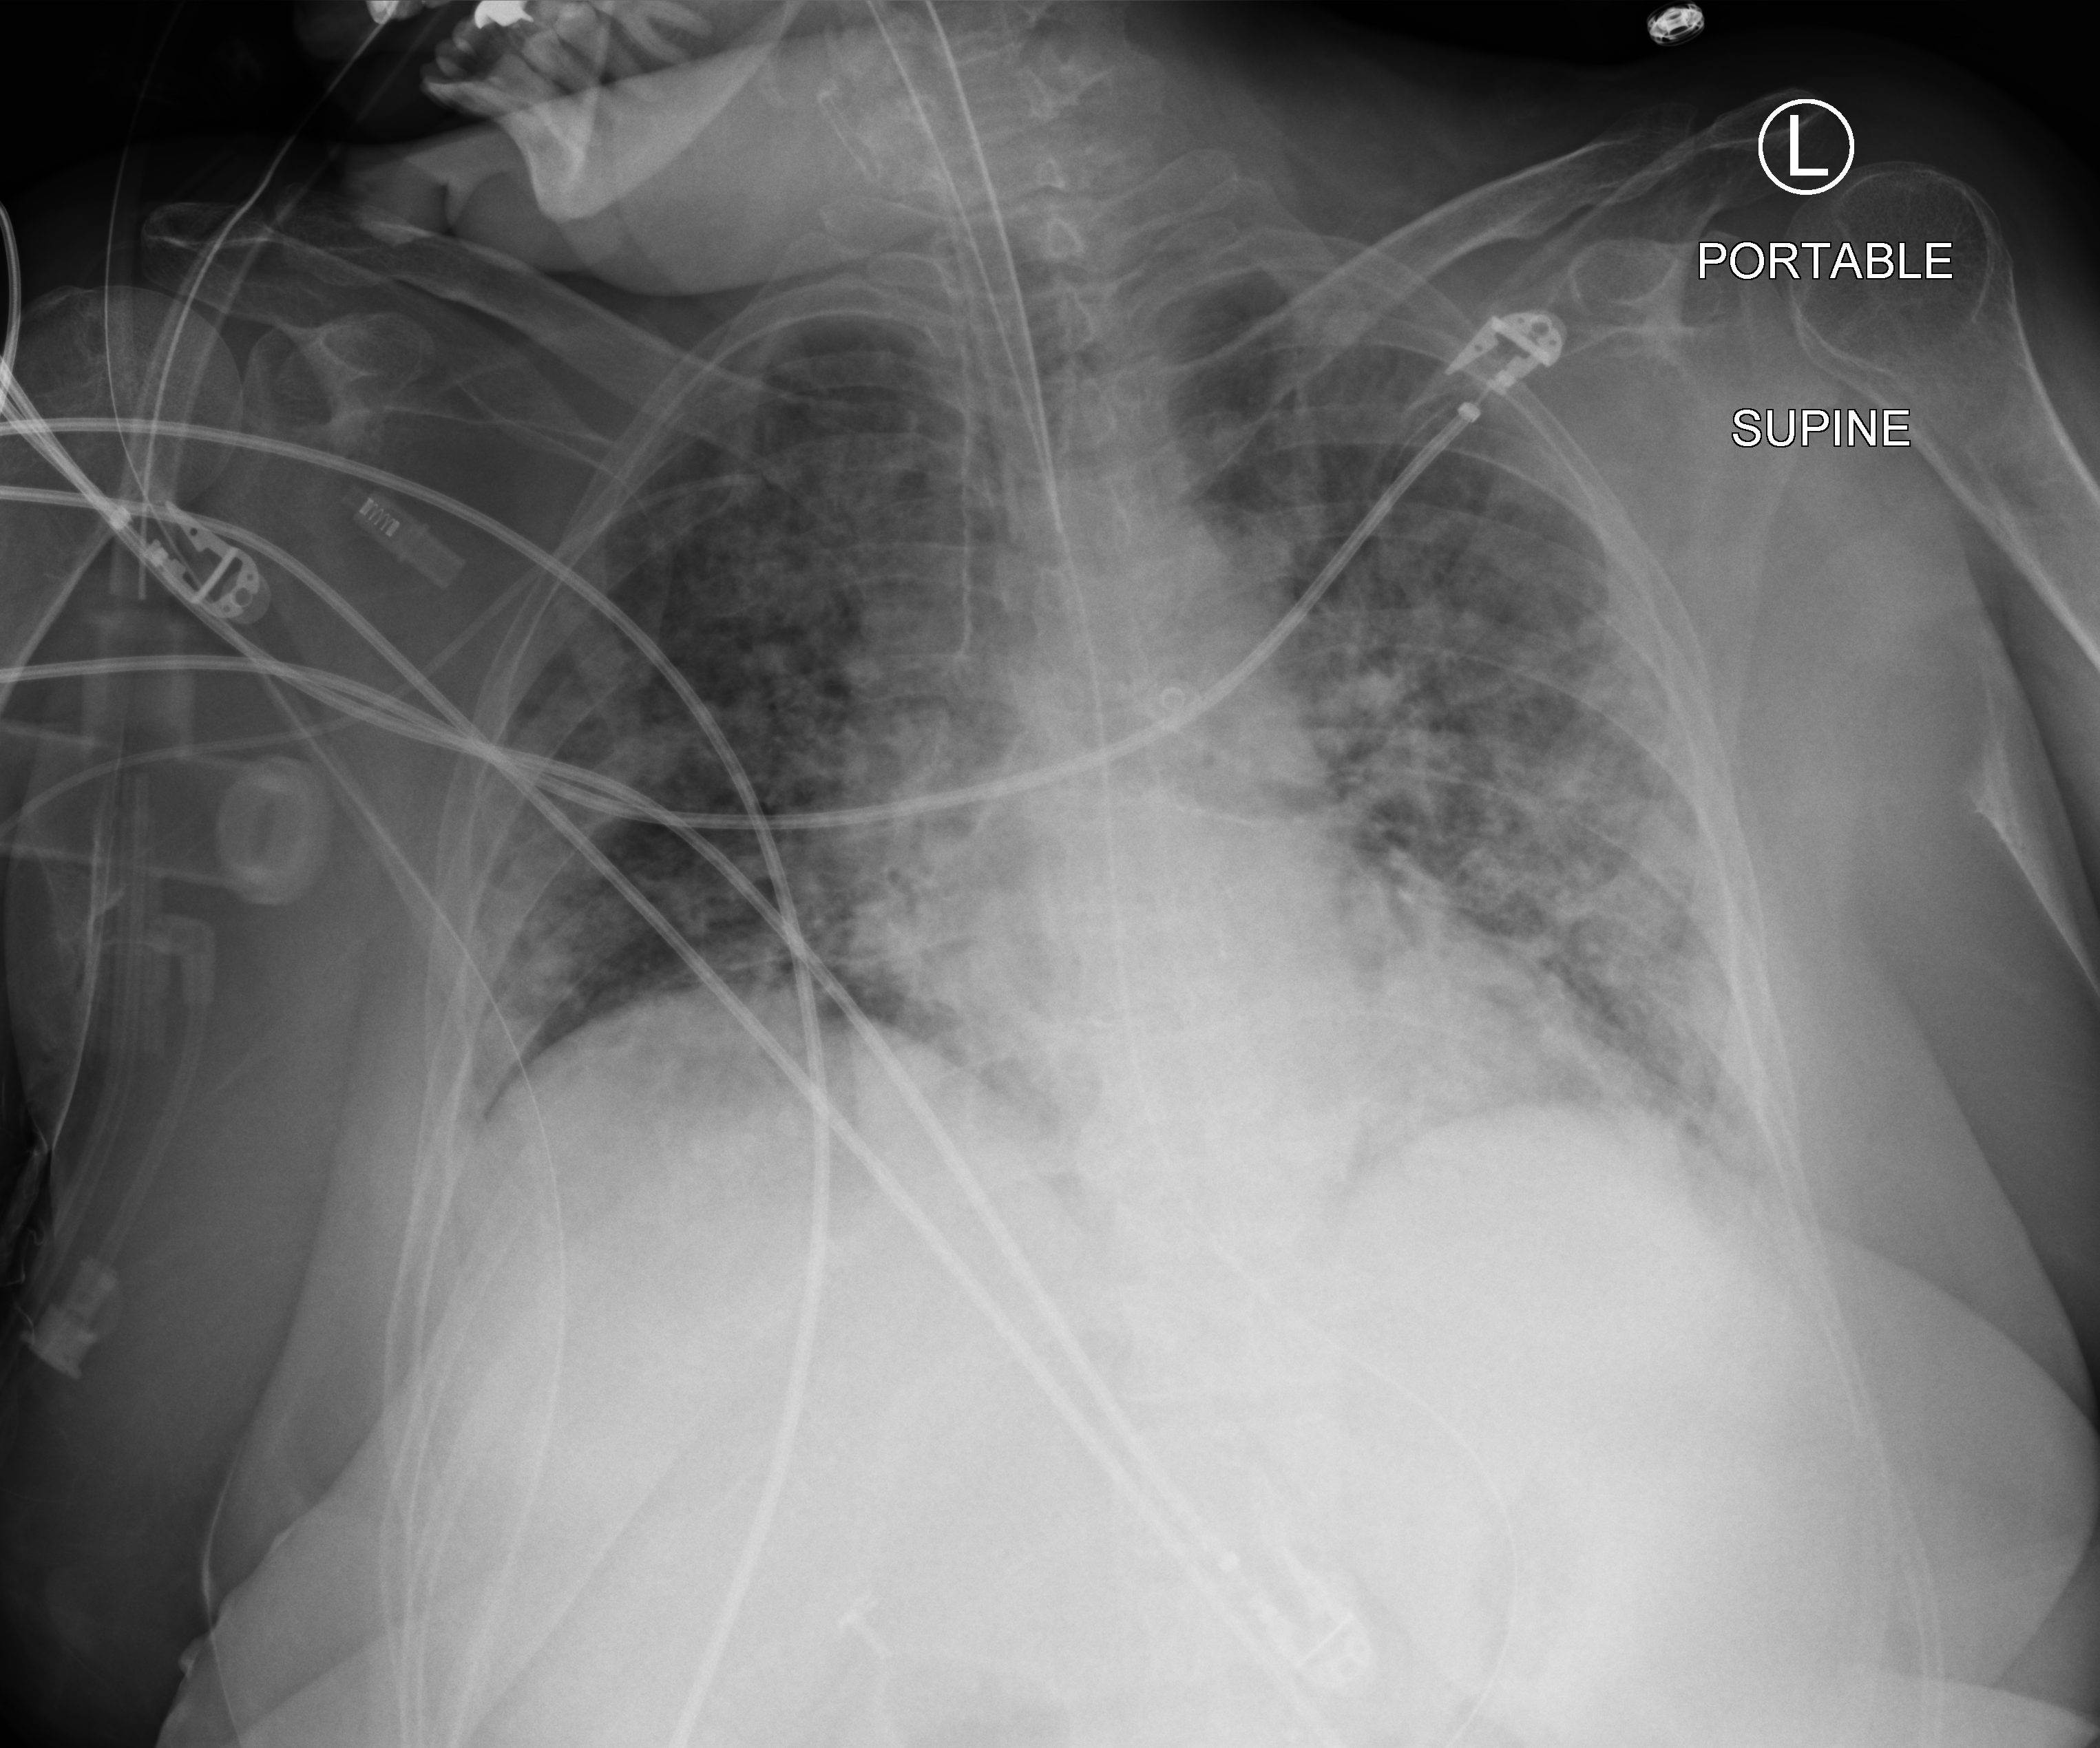
Bedside chest radiograph (computed radiography); anteroposterior (AP) projection. Patient hospitalised with COVID-19; female, aged 18–59 years.
Admission-level facts for this patient (not findings on this image; timing relative to this image not recorded): admitted to intensive care during this hospital stay: yes; hypertension (admission record): no.